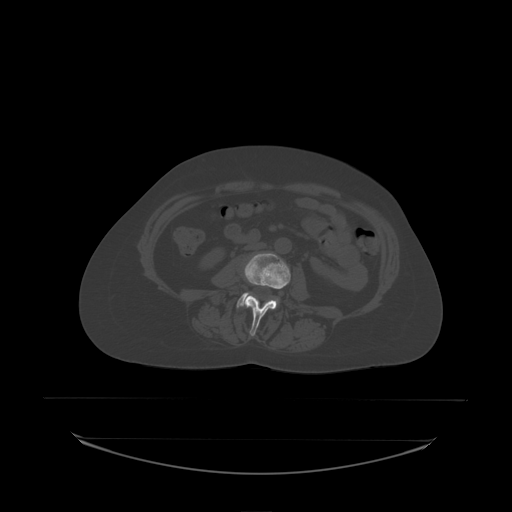
CT including the spine, one axial slice. Slice 58 of 242 in the series (ordered by position). Bone window (W 1800 / L 400 HU). 2.5 mm slice thickness. 512 × 512 image matrix, field of view 500 × 500 mm. Patient: female, 53 years. From the clinical record (not read from this slice): primary cancer: lung; vertebrae with lytic lesions (as recorded): T7, L1.
Annotated regions visible in this slice (semi-automatically segmented with operator editing):
- L3 vertebra: box from (x=244, y=253) to (x=291, y=337) px
- L4 vertebra: (x=237, y=292)–(x=279, y=308)